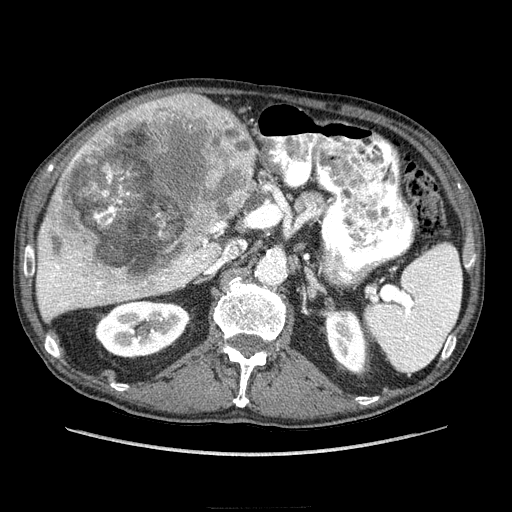
Contrast-enhanced abdominal CT (liver protocol), one axial slice; slice 137 of 218 in the series (ordered by position); reconstruction kernel STANDARD; 100 kVp; soft-tissue window (W 400 / L 40 HU); 2.5 mm slice thickness; 512 × 512 image matrix, field of view 380 × 380 mm. From the clinical record (not read from this slice): diagnosis: hepatocellular carcinoma (patient treated with transarterial chemoembolisation; whether this scan precedes or follows treatment is not stated here); TNM stage (as recorded): Stage-IIIA; Child-Pugh class: A; tumour differentiation: well differentiated; tumour nodularity: multinodular.
Annotated regions visible in this slice (semi-automatically segmented with operator editing):
- liver parenchyma outside the tumour (the mass and vessels are separate outlines, so this box may not span the whole liver): bounding box <36,100,256,320> (left, top, right, bottom; pixels)
- mass: <38,91,256,289>
- liver vessels: <38,263,190,310>